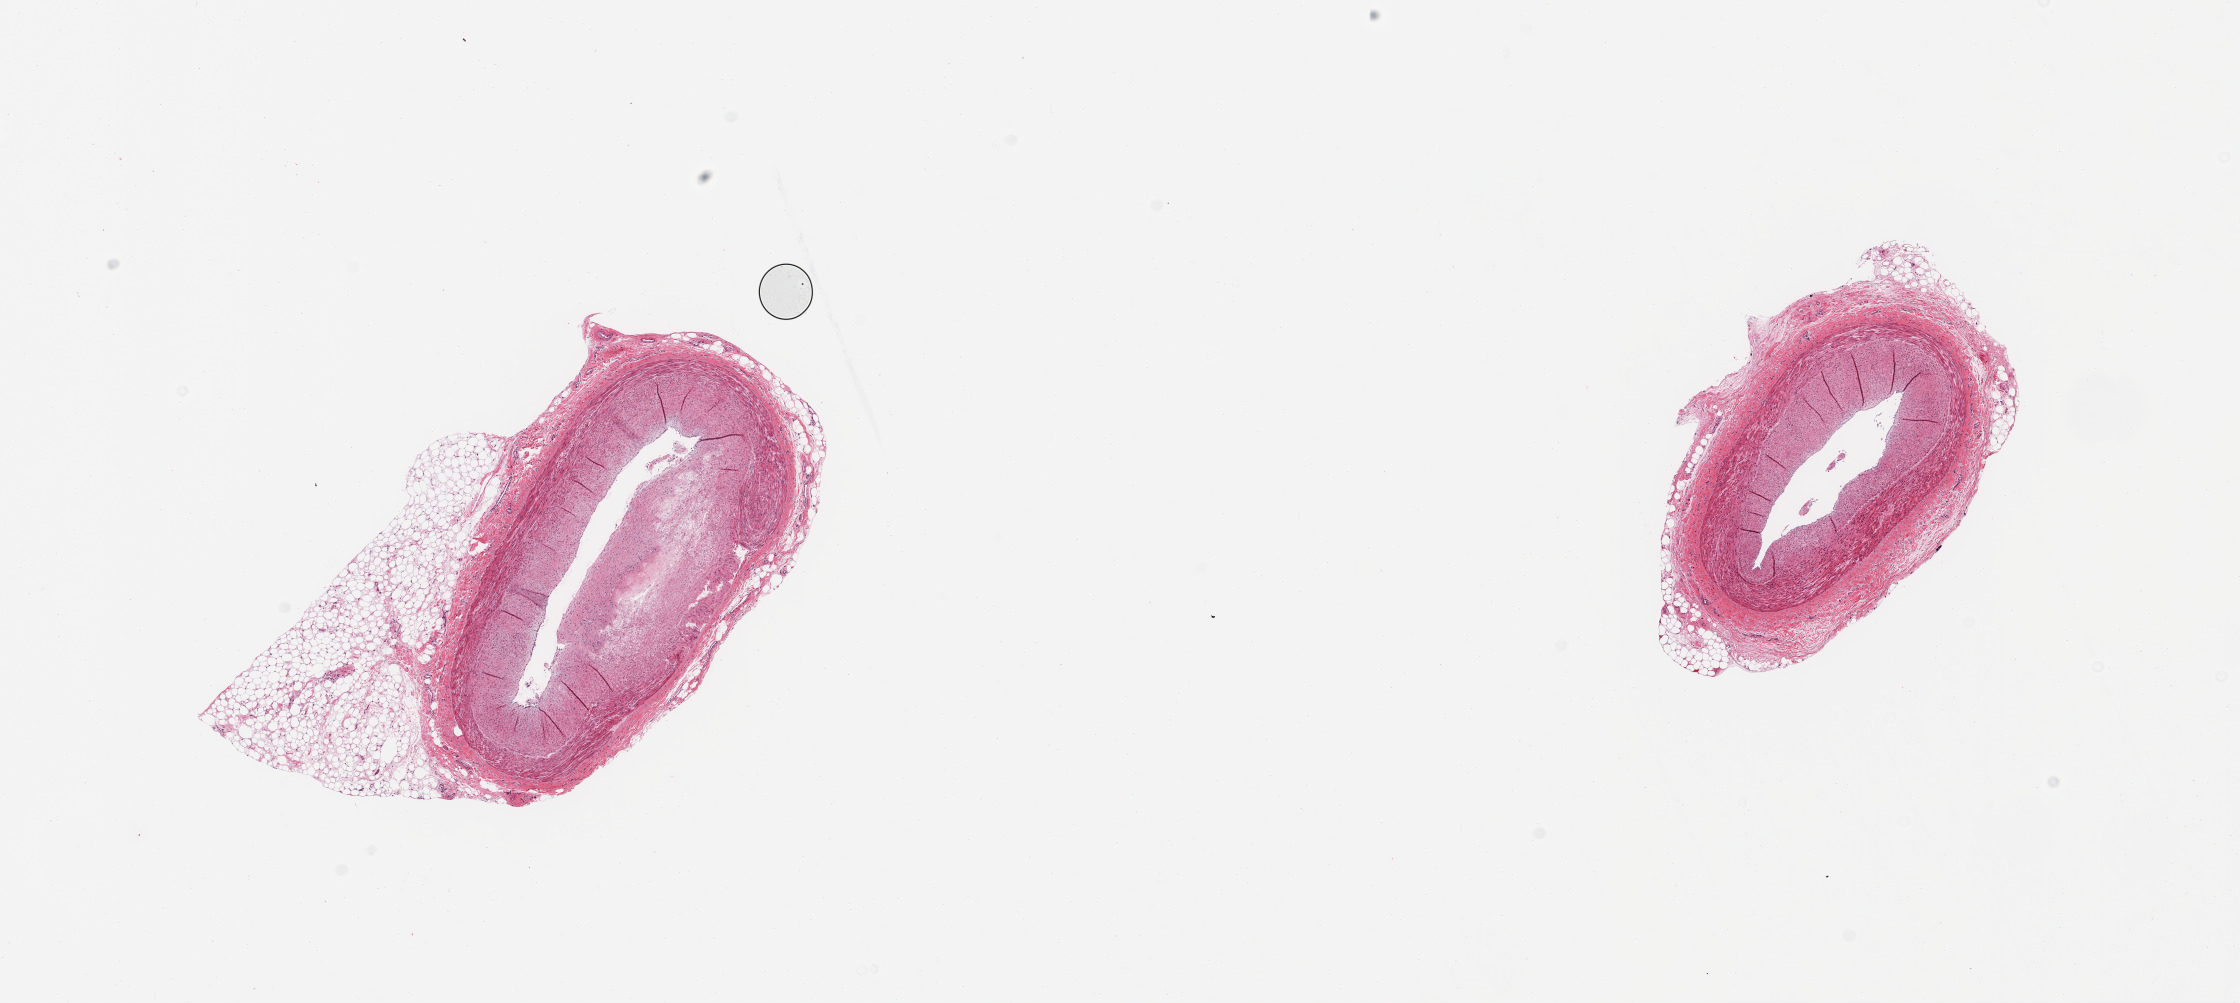
Whole-slide image, hematoxylin and eosin (H&E) stain, a low-resolution overview of the entire scanned area, about 17.7 x 7.9 mm (slide scanned at 20x); PAXgene-fixed, paraffin-embedded tissue; sampled site (target tissue): coronary artery; donor tissue sample. Donor: female.
Review note (as recorded): 2 pieces; moderately occlusive fibroatheromatous plaque; 1 piece has 40% untrimmed external adipose content.